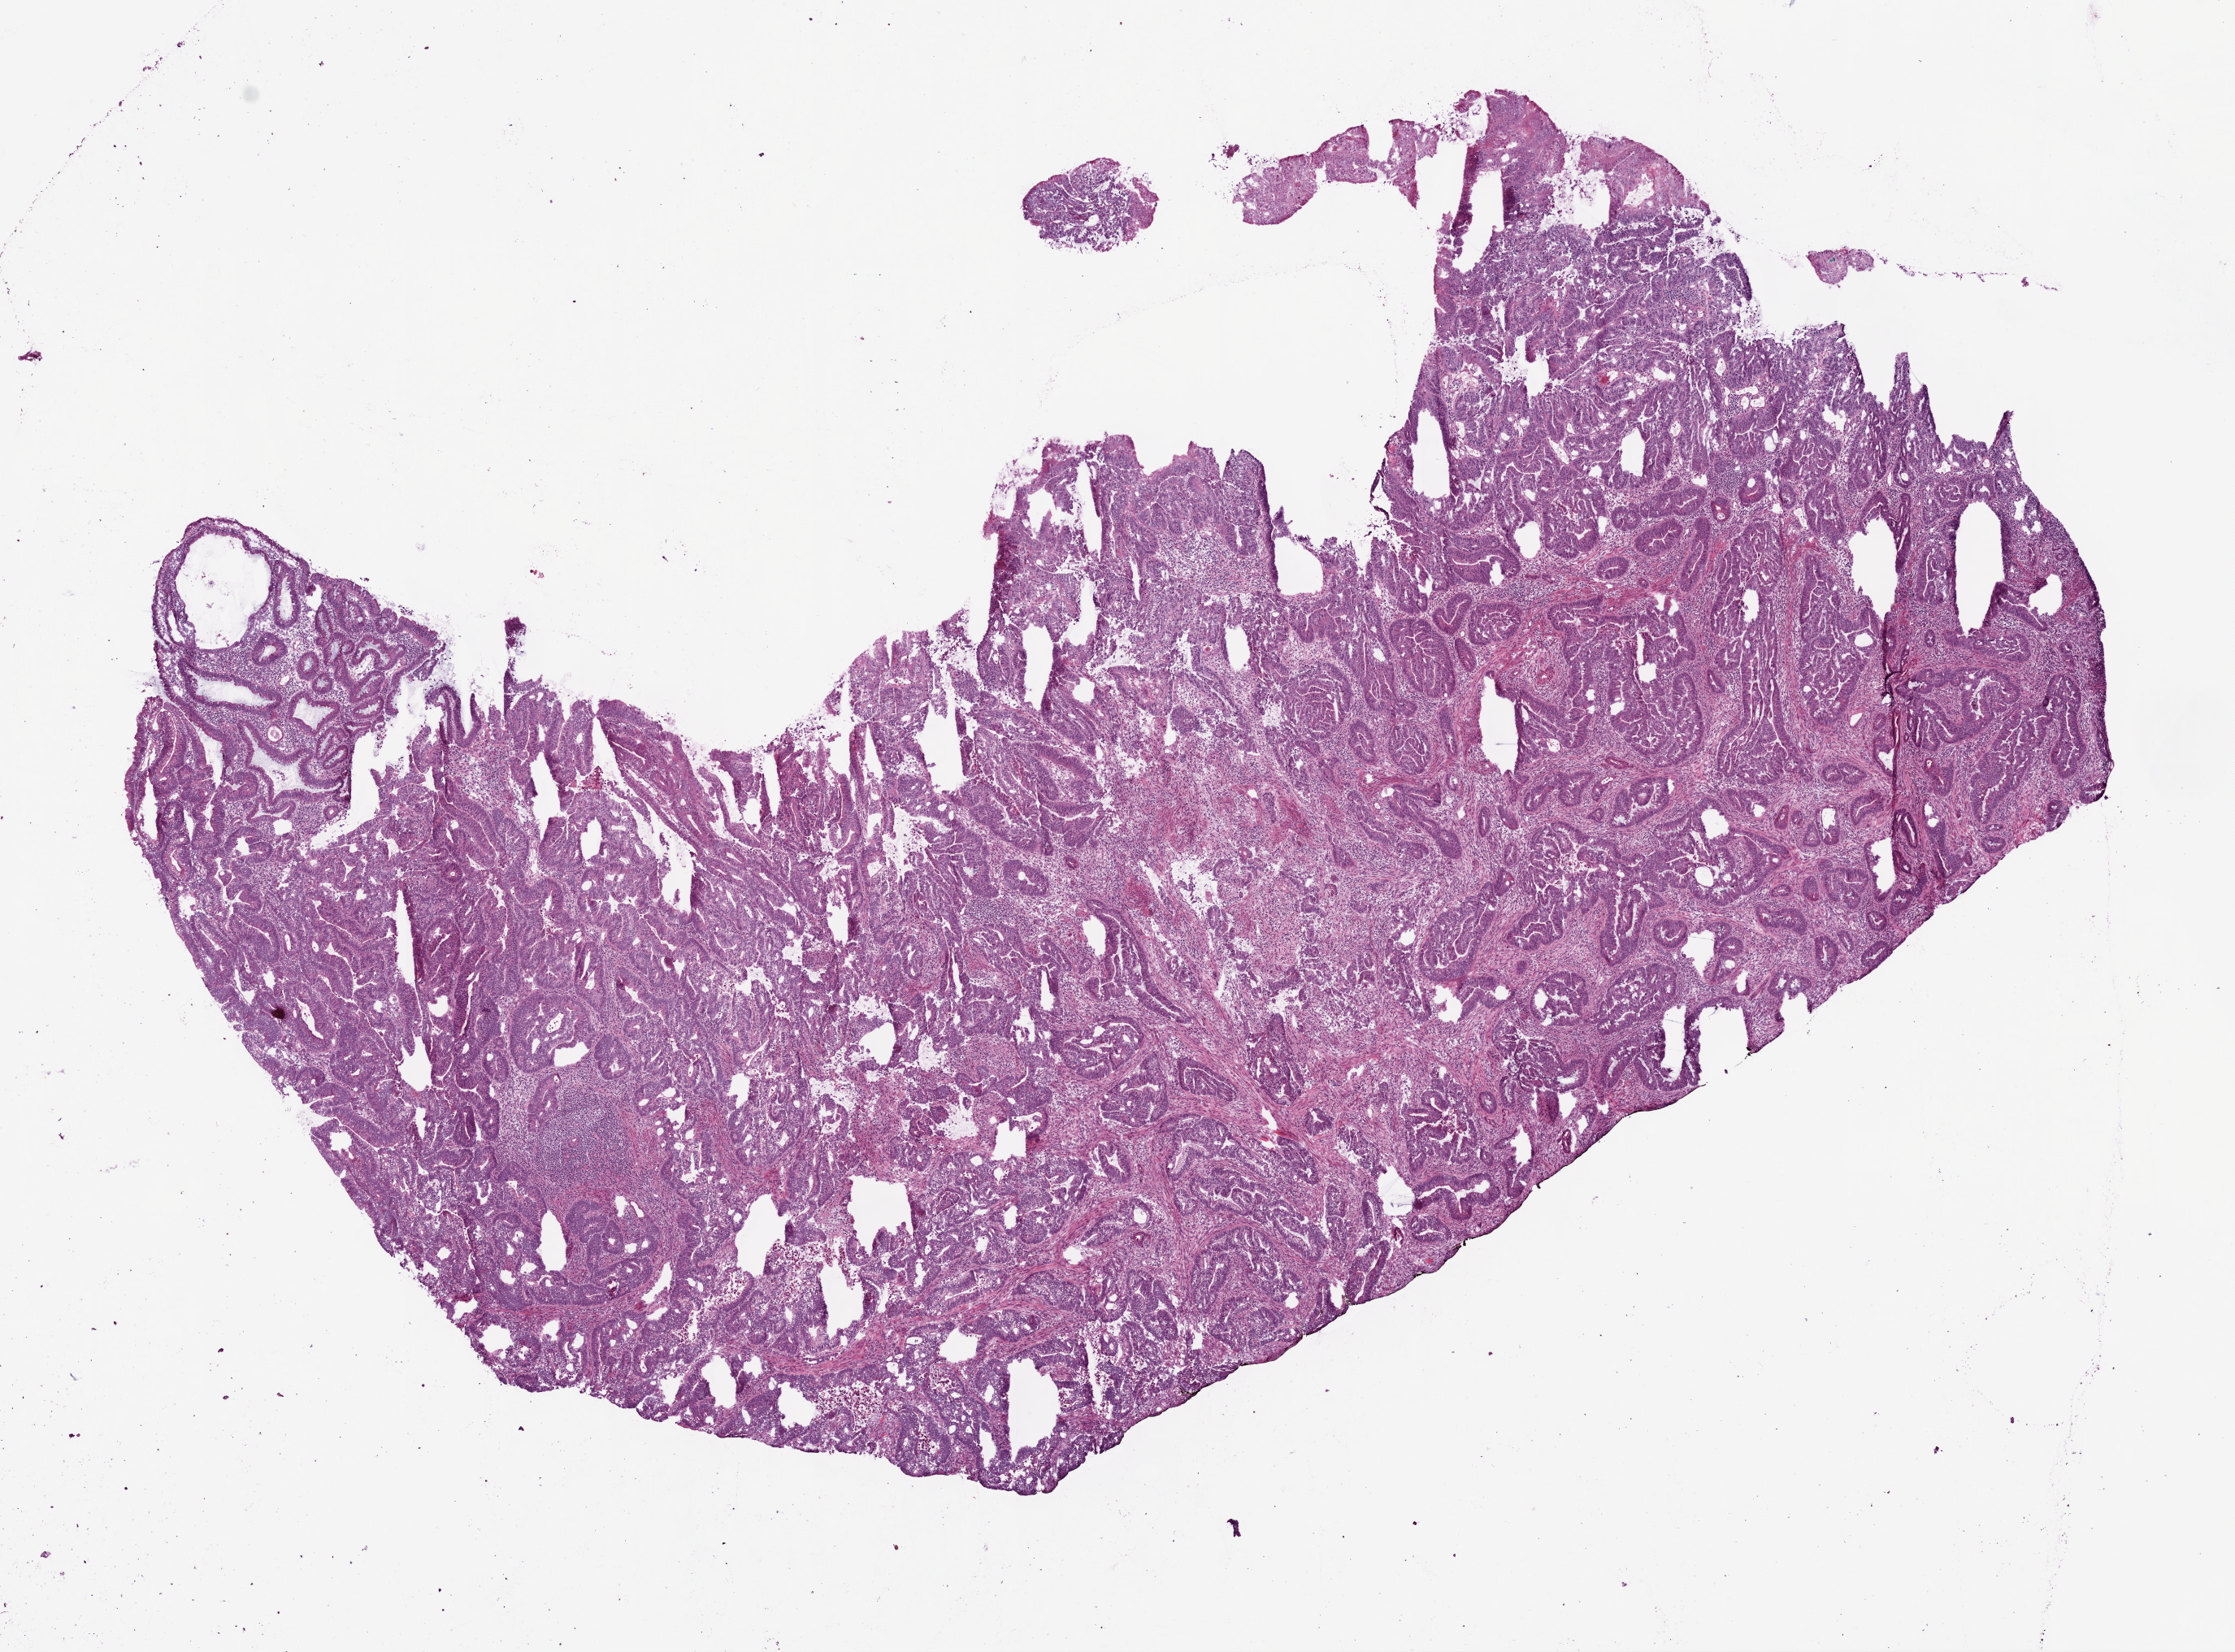
Digitized H&E tissue section (whole slide) — low-resolution overview of the scanned area, about 11.0 x 8.2 mm (from a 20x scan); frozen section from the bottom of the tissue portion; colon, primary tumour sample. Patient: female, age at initial diagnosis 57 years. Pathologist review of this section (percent, as recorded): tumour cells 65%, tumour nuclei 70%.
Pathologic diagnosis: Adenocarcinoma, NOS (ascending colon).